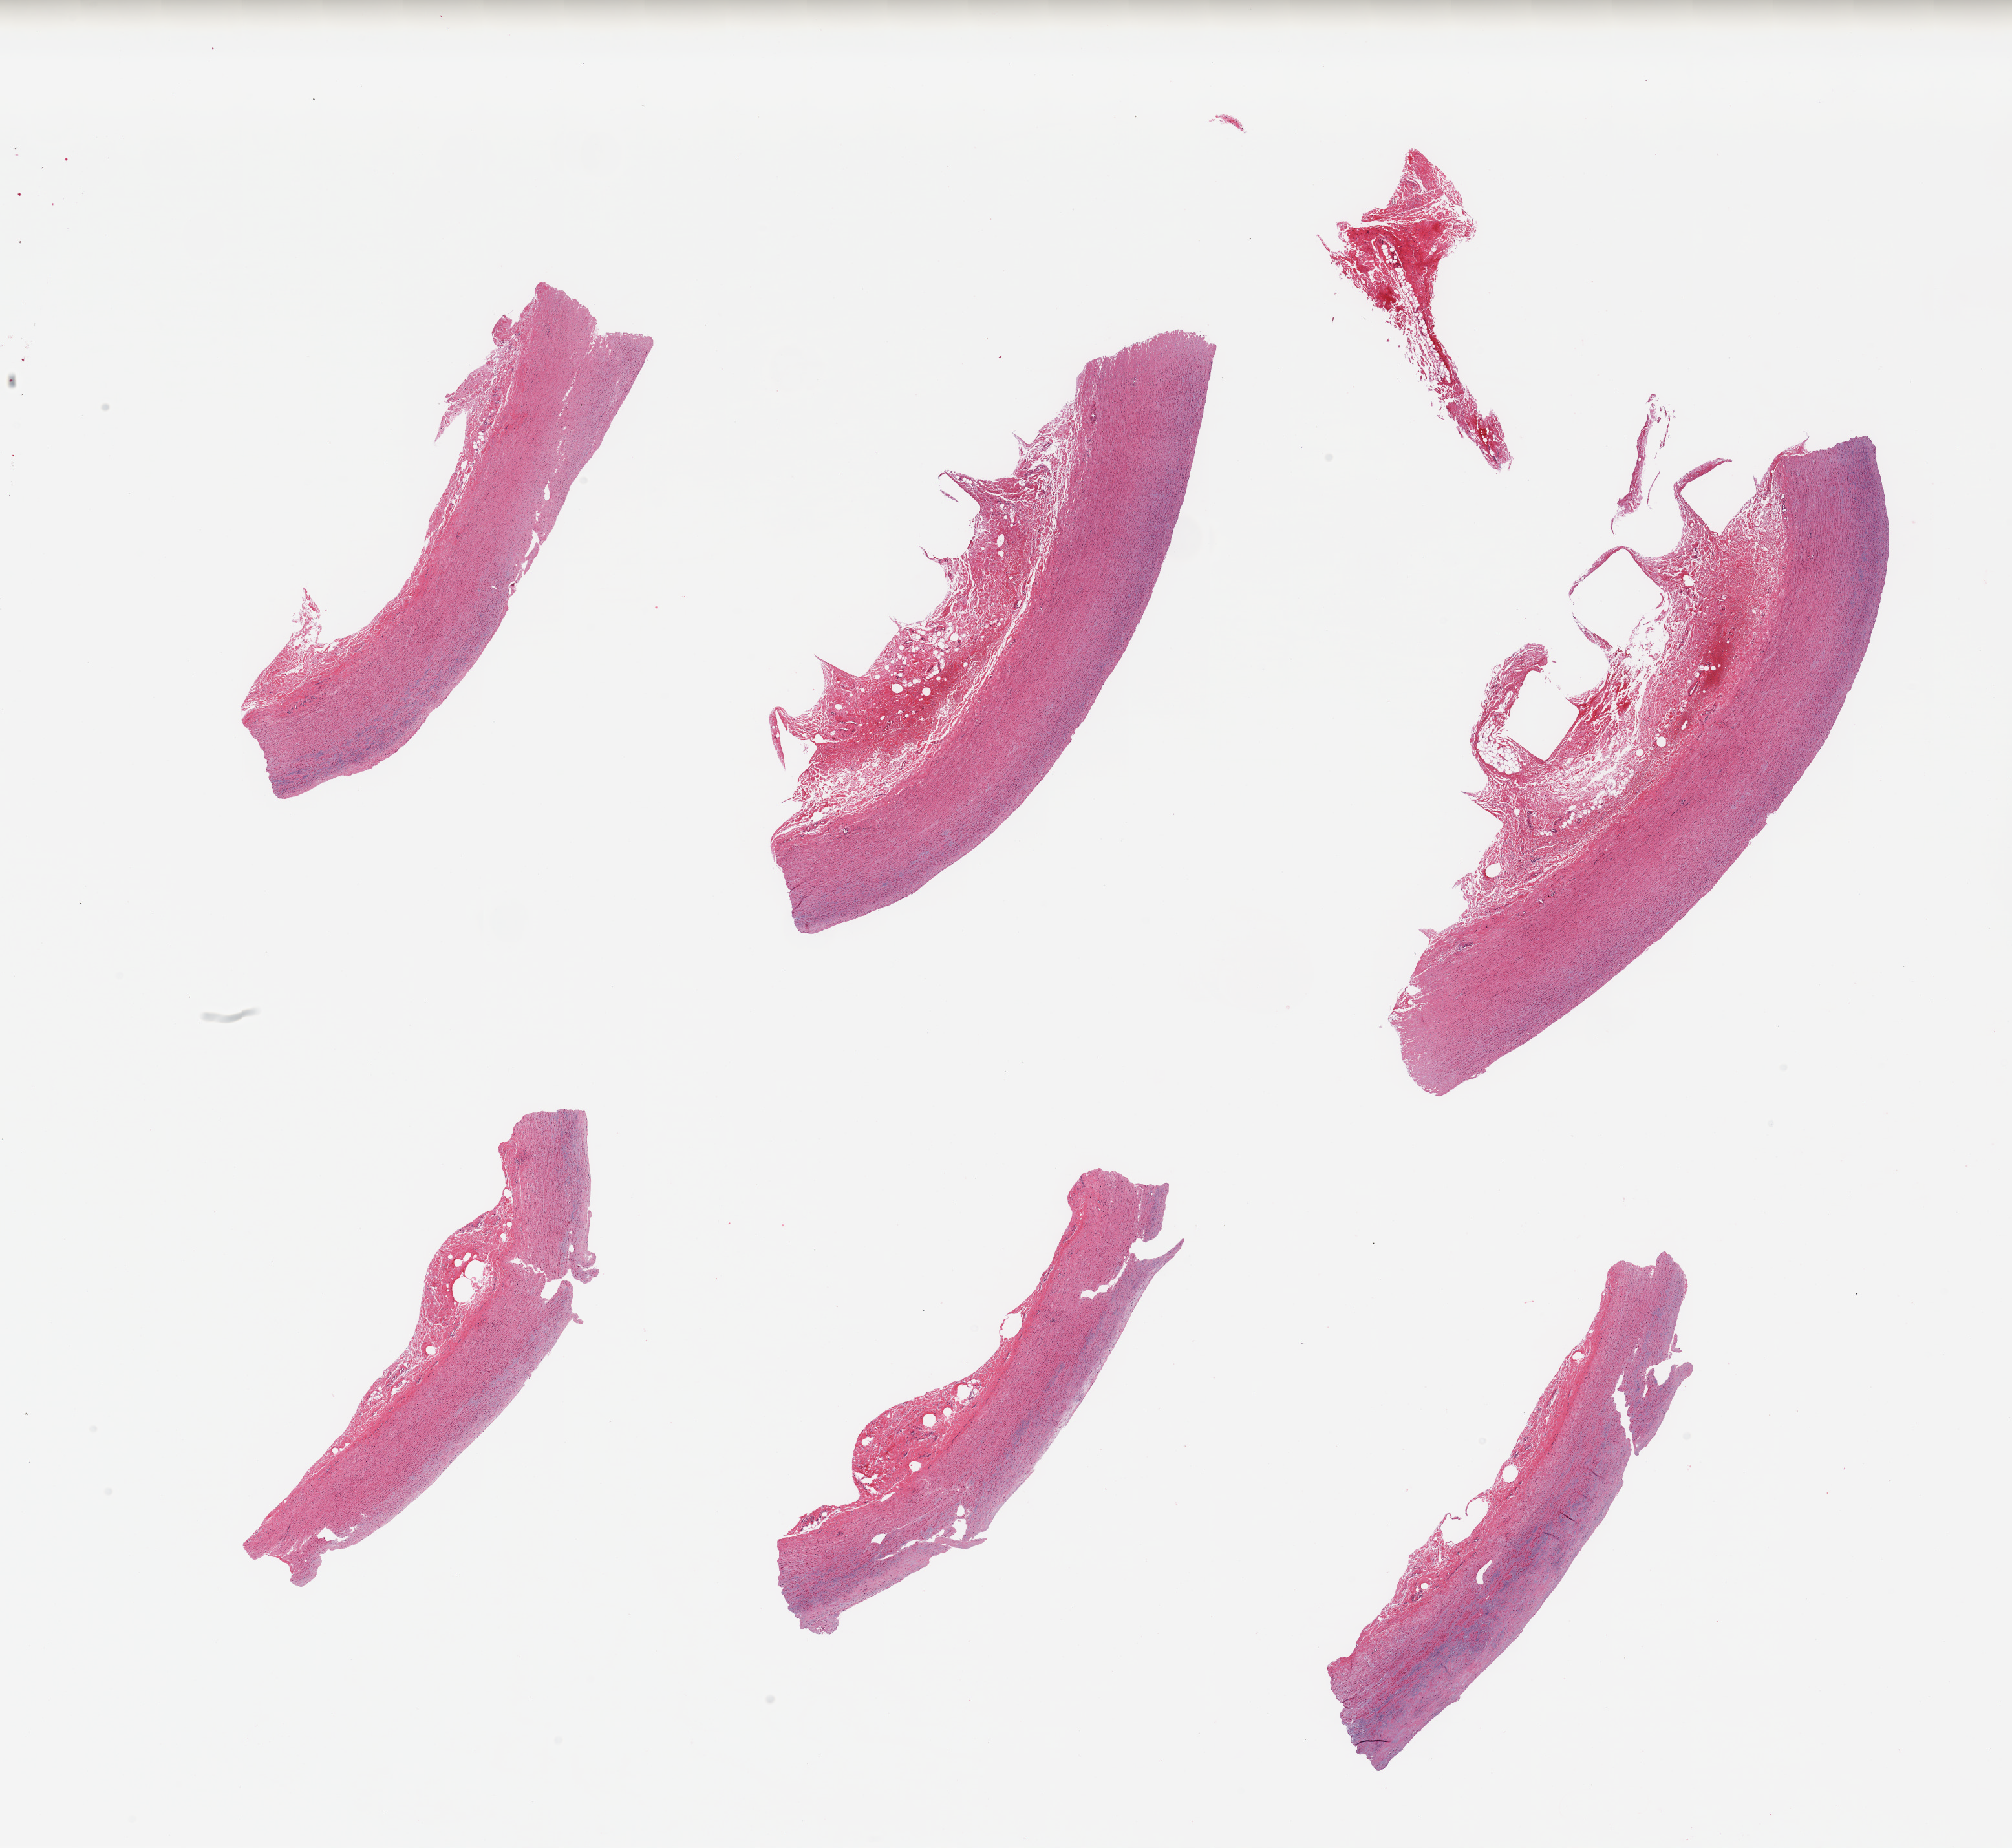
Hematoxylin and eosin (H&E) whole-slide image, low-resolution overview of the scanned area, about 24.6 x 22.6 mm. PAXgene-fixed, paraffin-embedded tissue. Section of aorta (target tissue). Donor tissue sample. Donor: male.
Review note (as recorded): 6 pieces, trace atherosis; adherent tages of serosa/fat up to ~1.3mm.